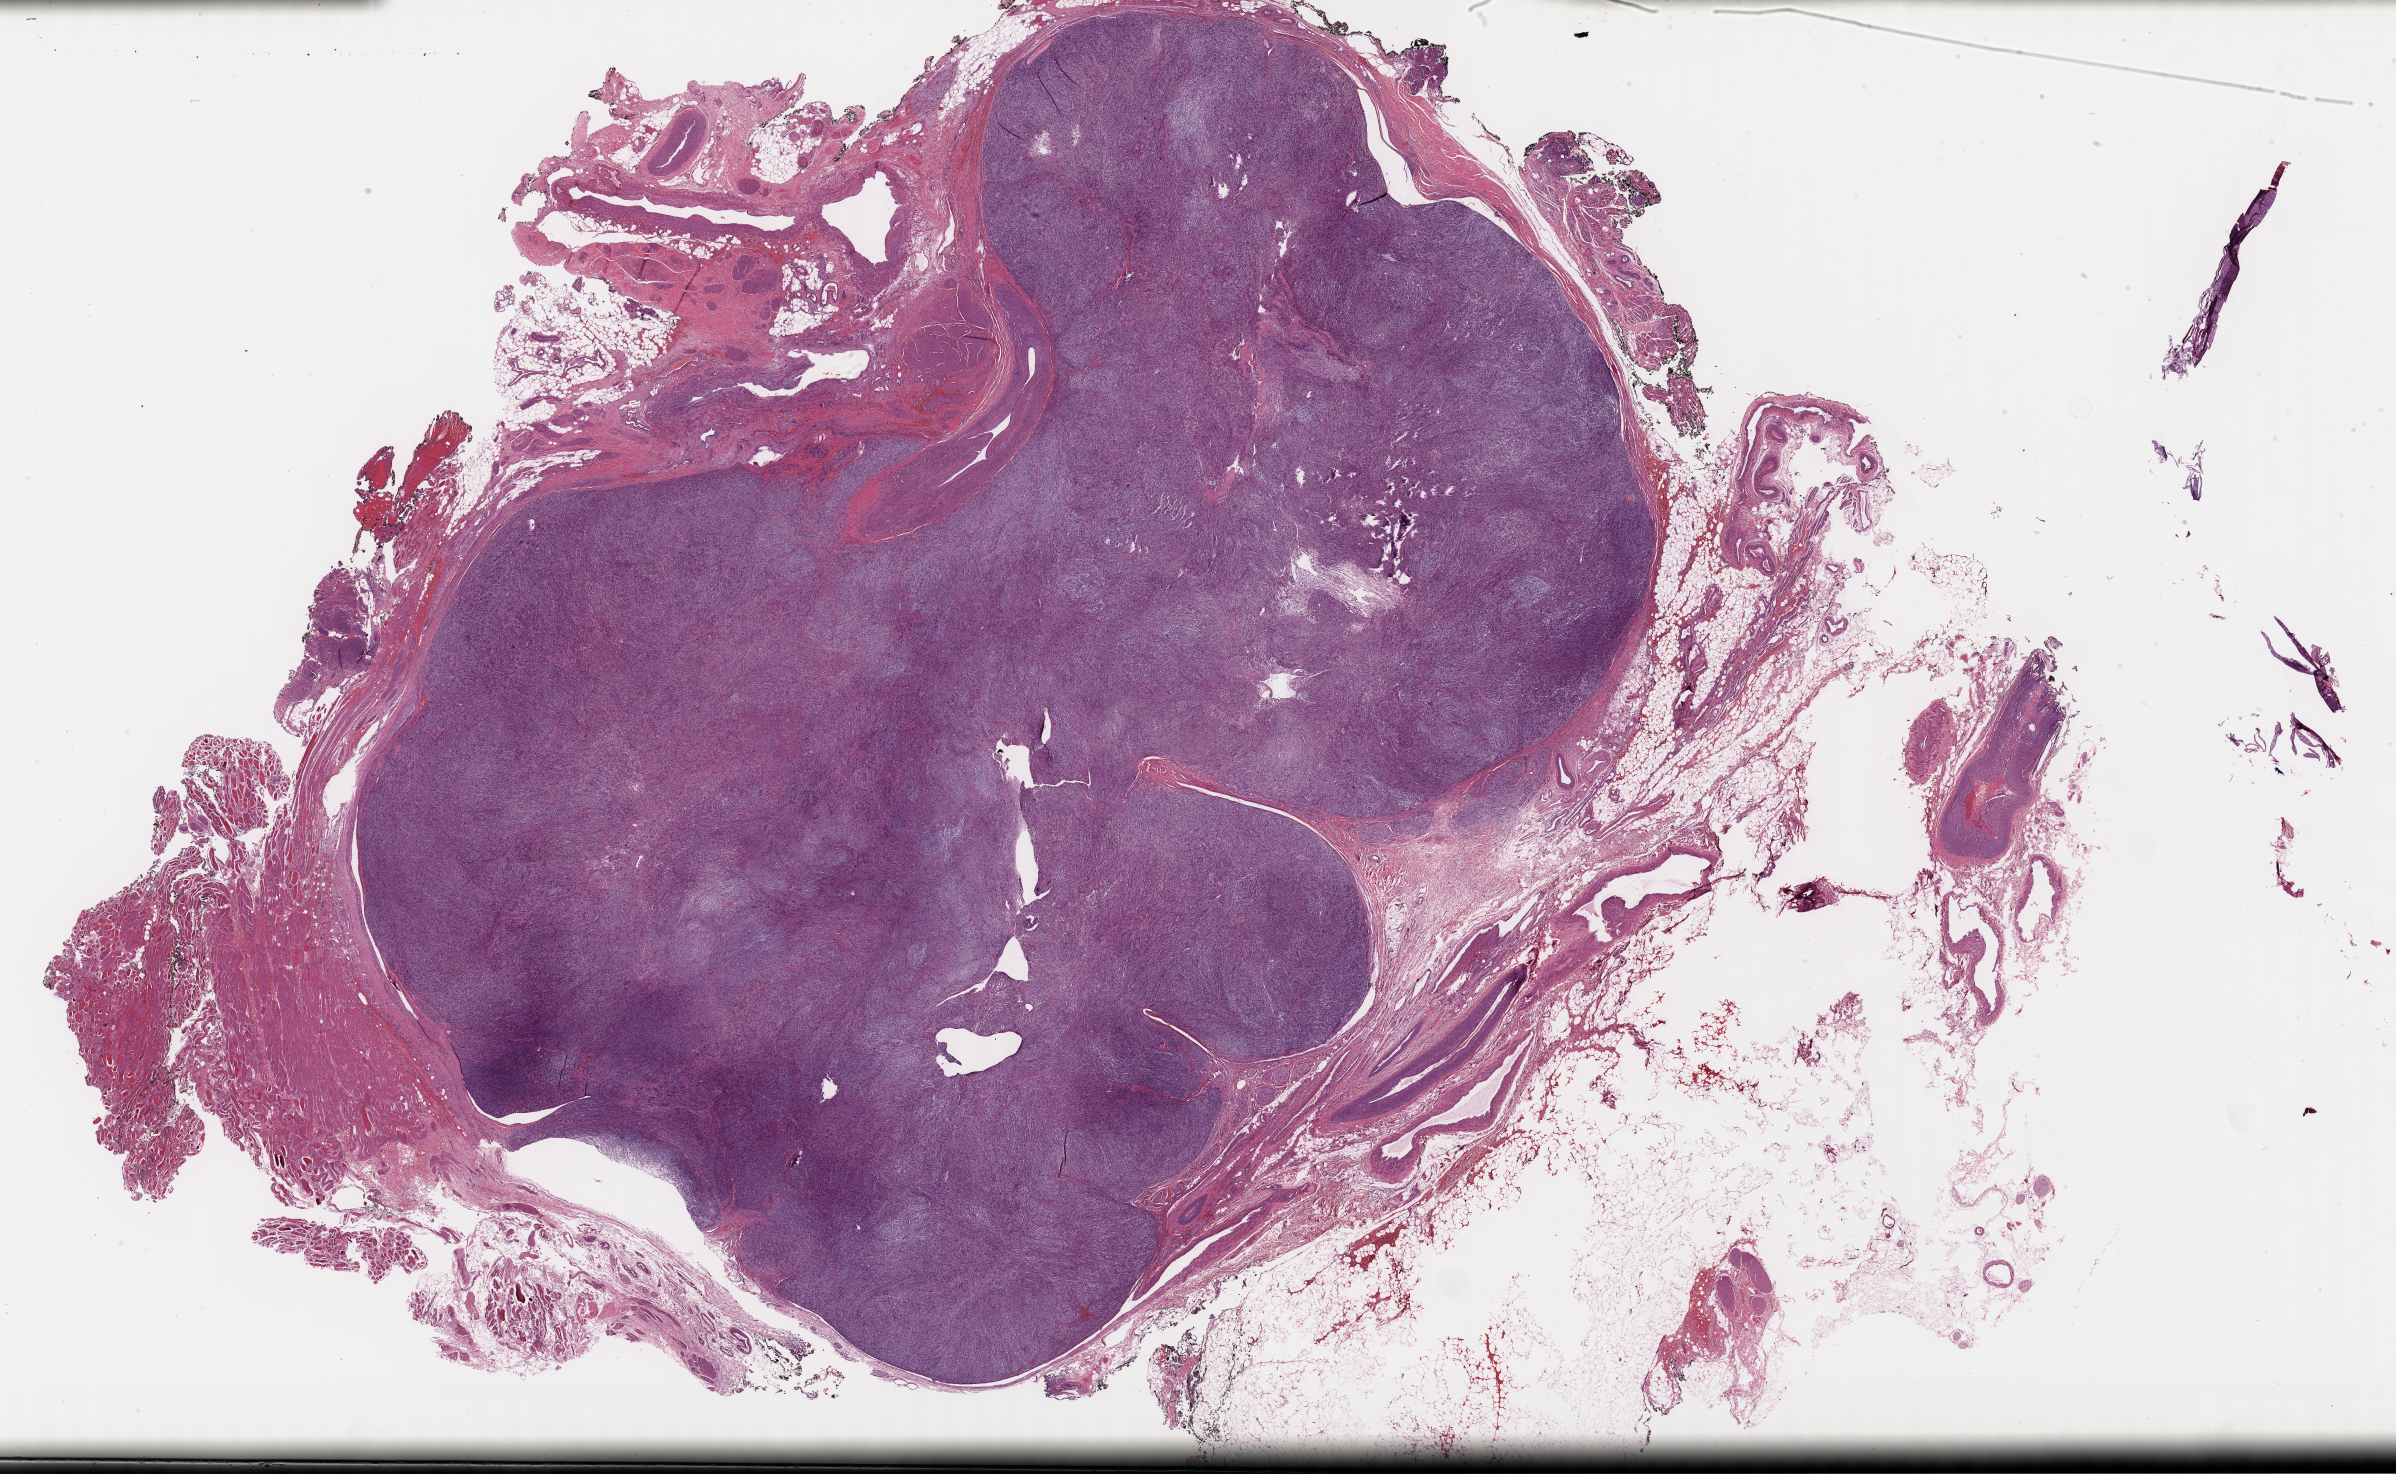
Whole-slide histology image, Hematoxylin and eosin (H&E) stained, whole scanned area (about 38.8 x 23.8 mm) shown as a low-resolution overview, formalin-fixed paraffin-embedded (FFPE) diagnostic section, primary tumour sample from the retroperitoneum and peritoneum. Male patient; age at initial diagnosis 84 years.
Diagnosis: Leiomyosarcoma, NOS (retroperitoneum).